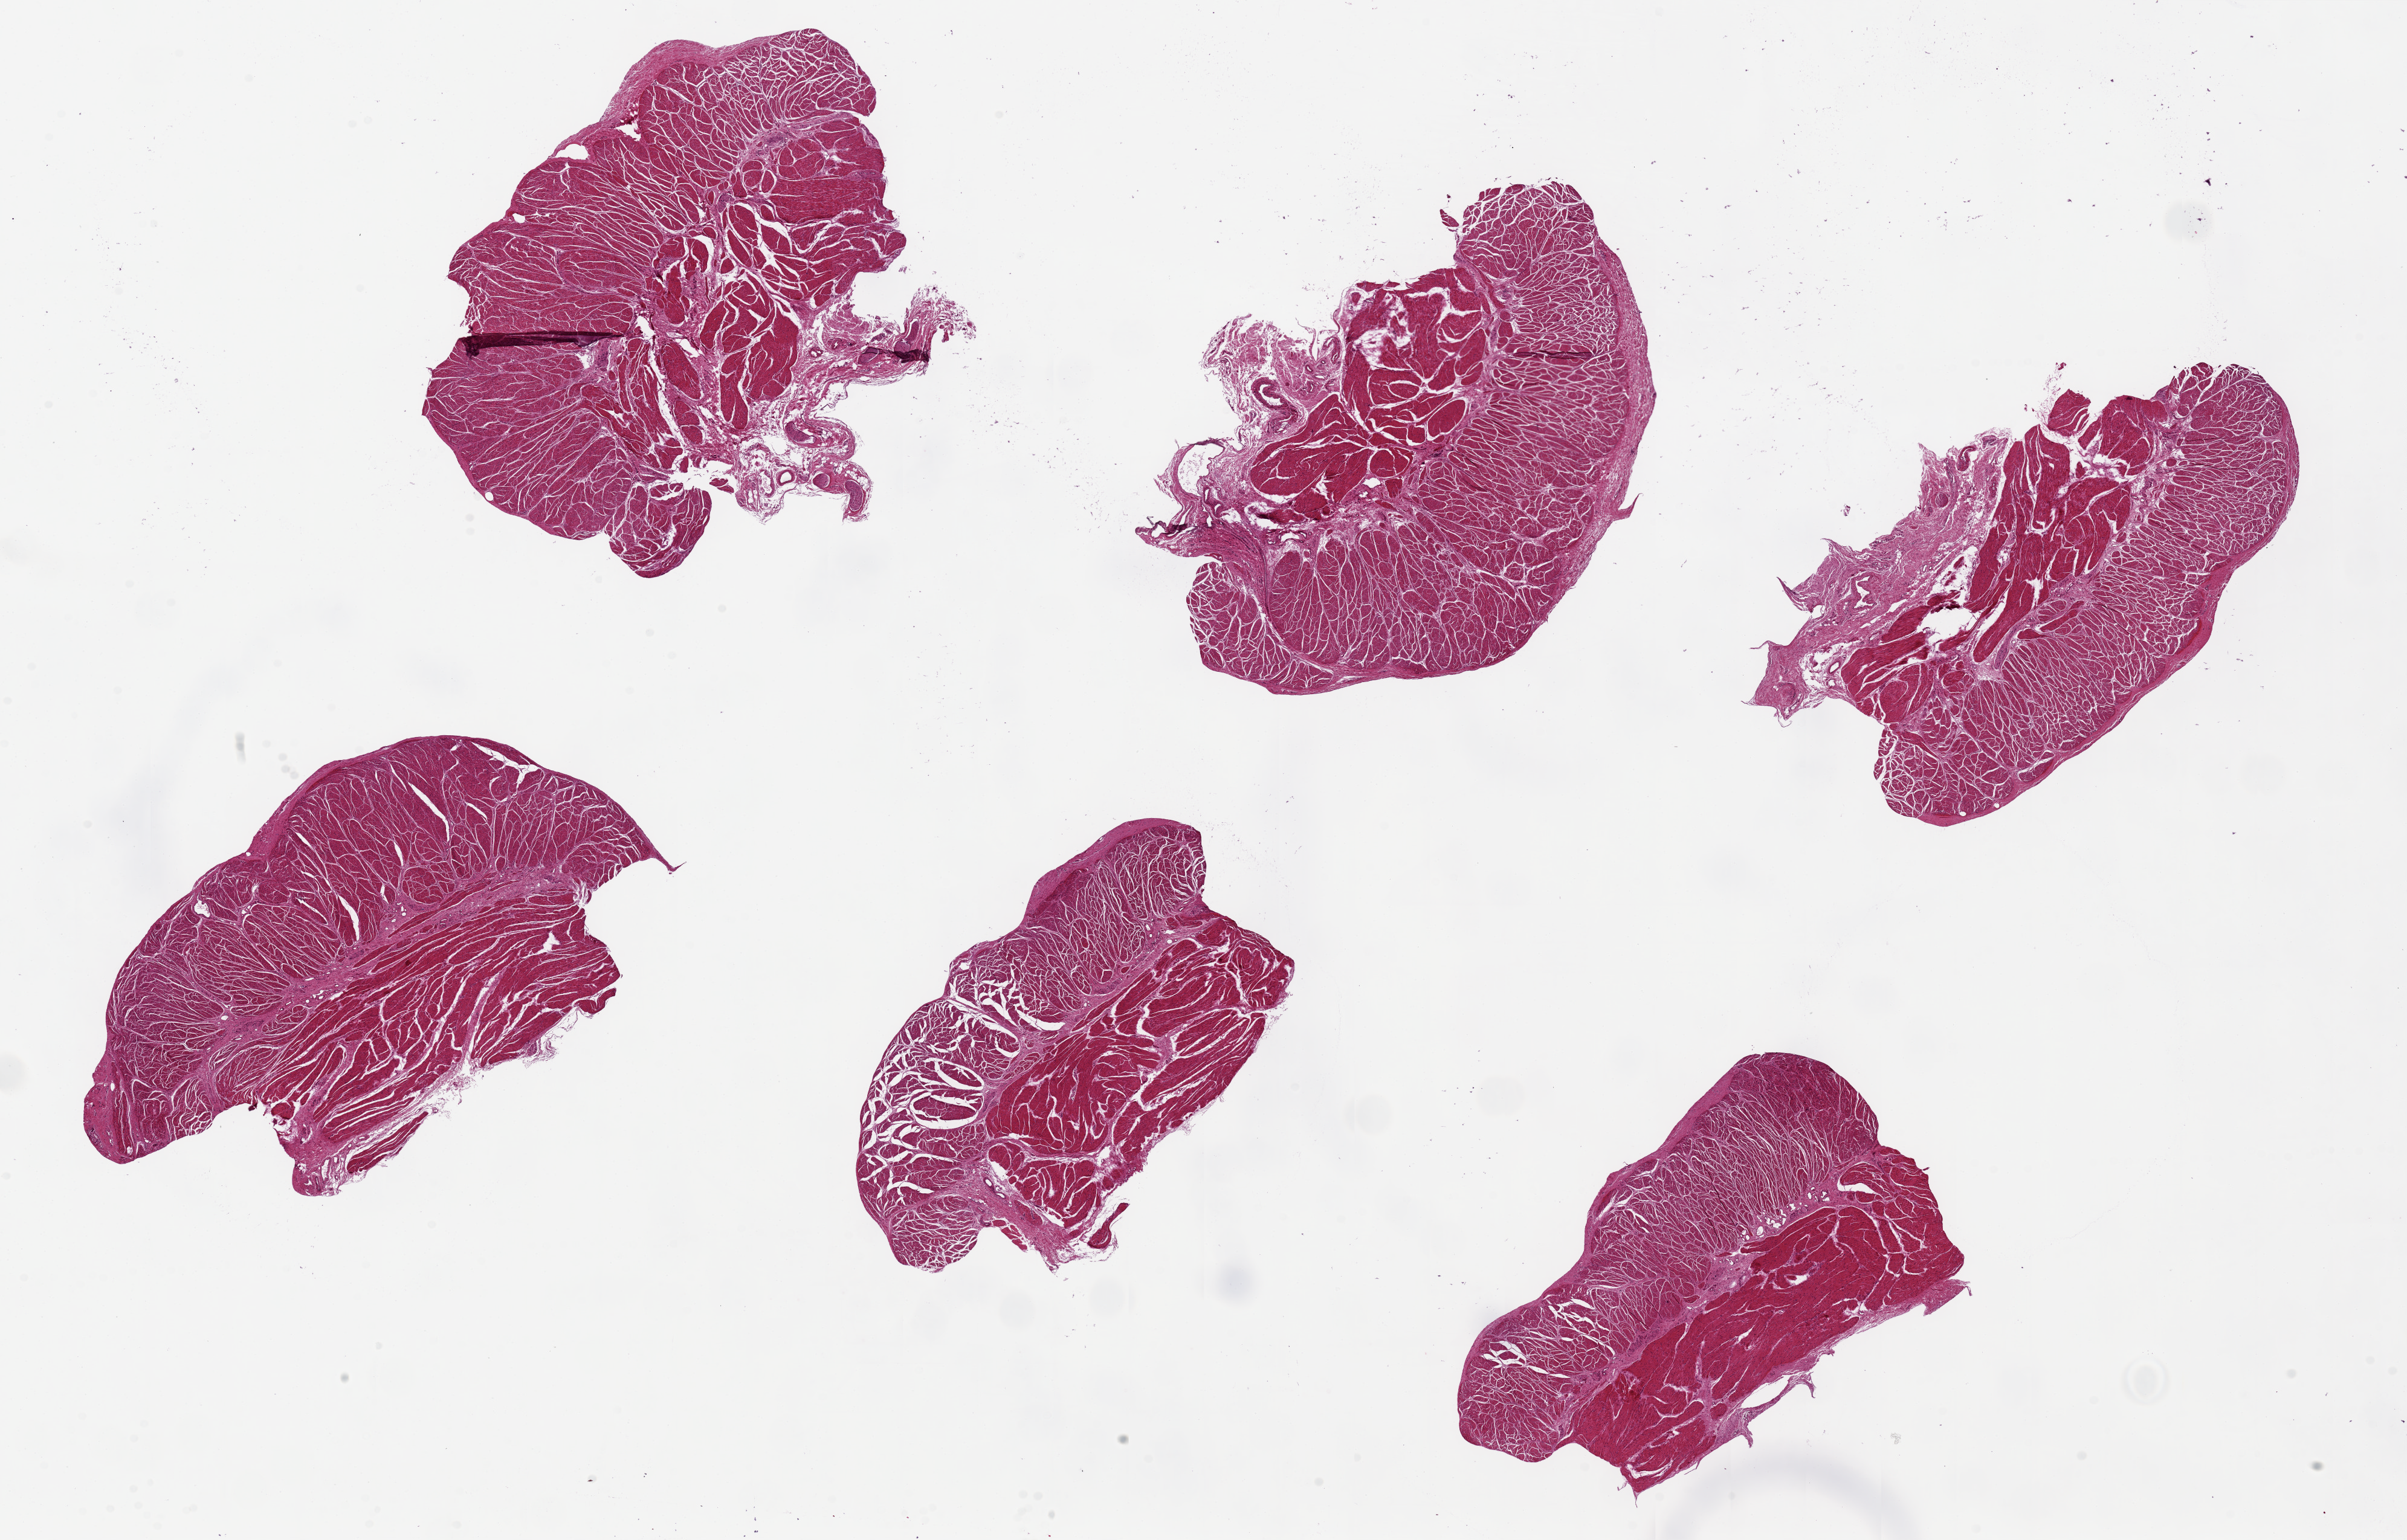
H&E whole-slide image, brightfield, whole scanned area (about 31.5 x 20.2 mm) shown as a low-resolution overview; PAXgene-fixed, paraffin-embedded tissue; target tissue: gastroesophageal junction; donor tissue sample. Female donor.
- review note (as recorded): 6 pieces, up to 8x5mm; well trimmed muscle